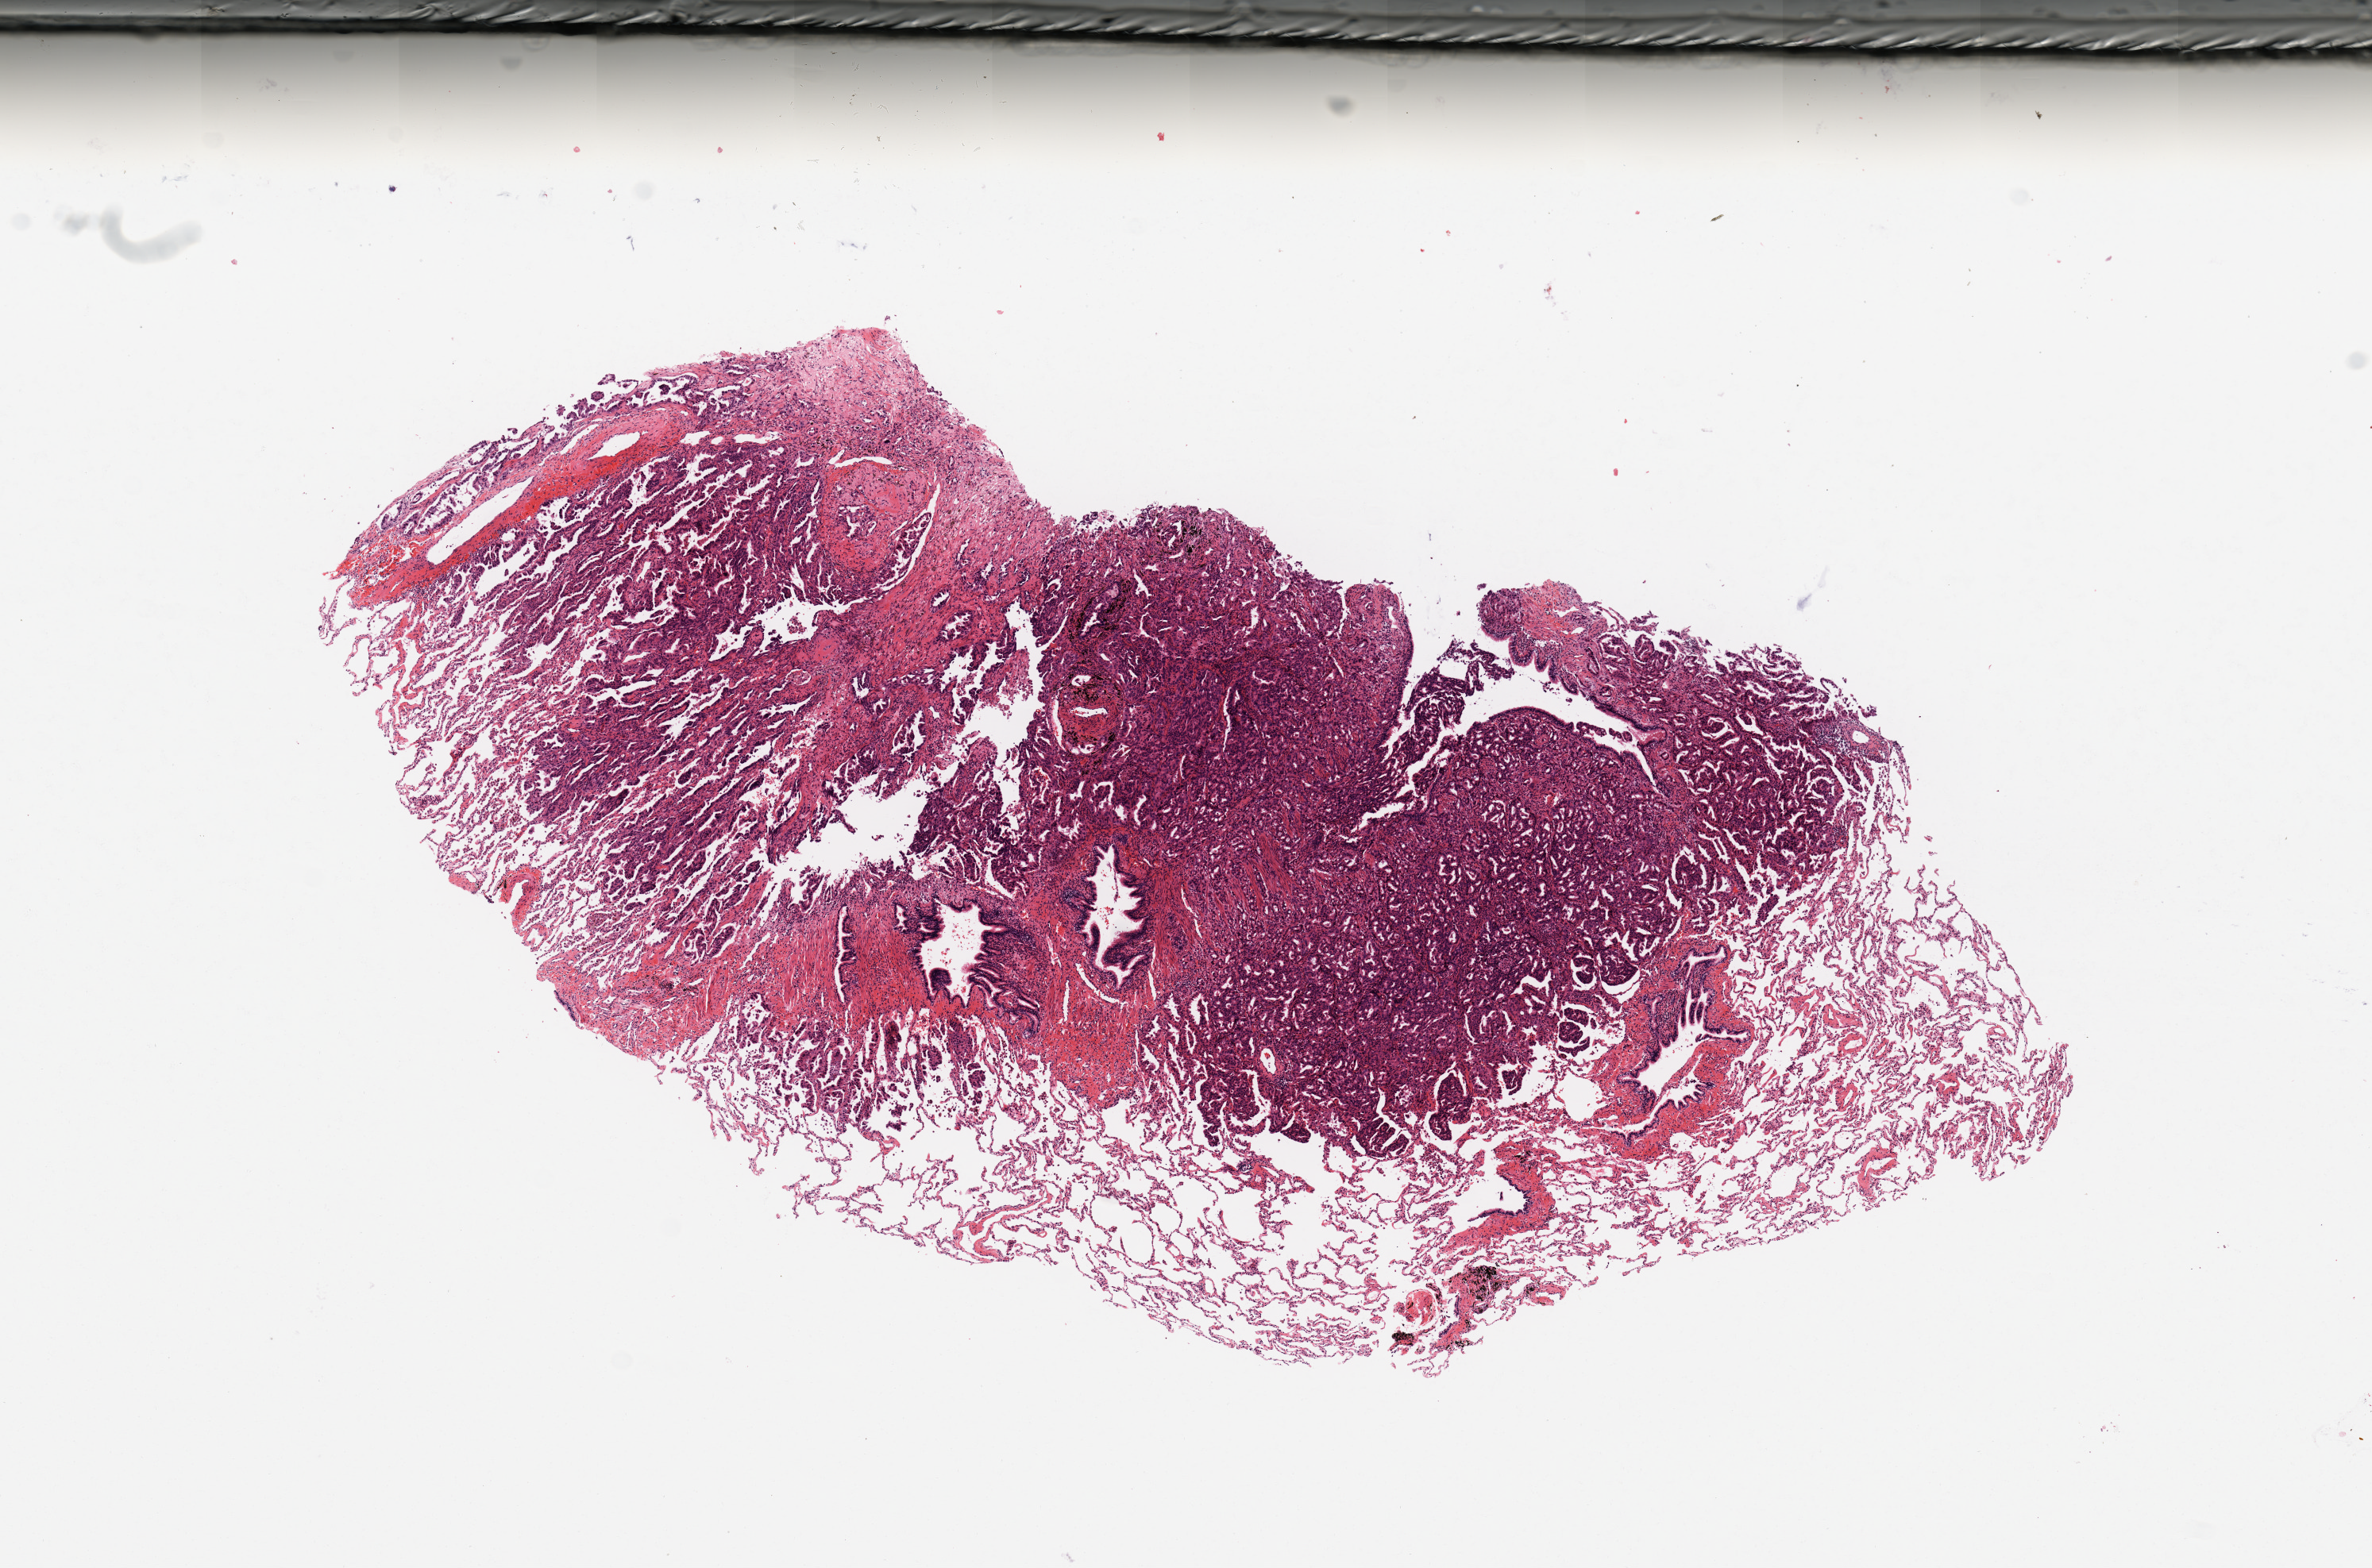
Whole-slide histology image, H&E, low-resolution overview of the scanned area, about 11.8 x 7.8 mm; tumour tissue sample, sampled site: lung. Patient: female, age 37 years. Histologic grade: G2 (moderately differentiated). Slide review estimates, as recorded: tumour nuclei 65%, necrosis 2%.
AJCC pathologic stage: IIIA. Primary tumour site (as recorded): left upper lobe. Diagnosis: Adenocarcinoma, NOS.